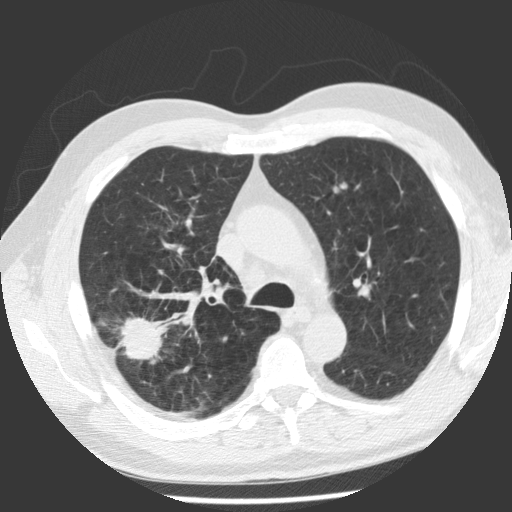
Low-dose screening chest CT, one axial slice; position 76 of 112 along the scan axis; reconstruction kernel STANDARD; 140 kVp; lung window (W 1500 / L -600 HU); 512 × 512 image matrix, field of view 344 × 344 mm.
Annotated regions visible in this slice (expert manual segmentation):
- lesion 1 (tumor, upper lobe of right lung): box from (x=119, y=317) to (x=163, y=360) px